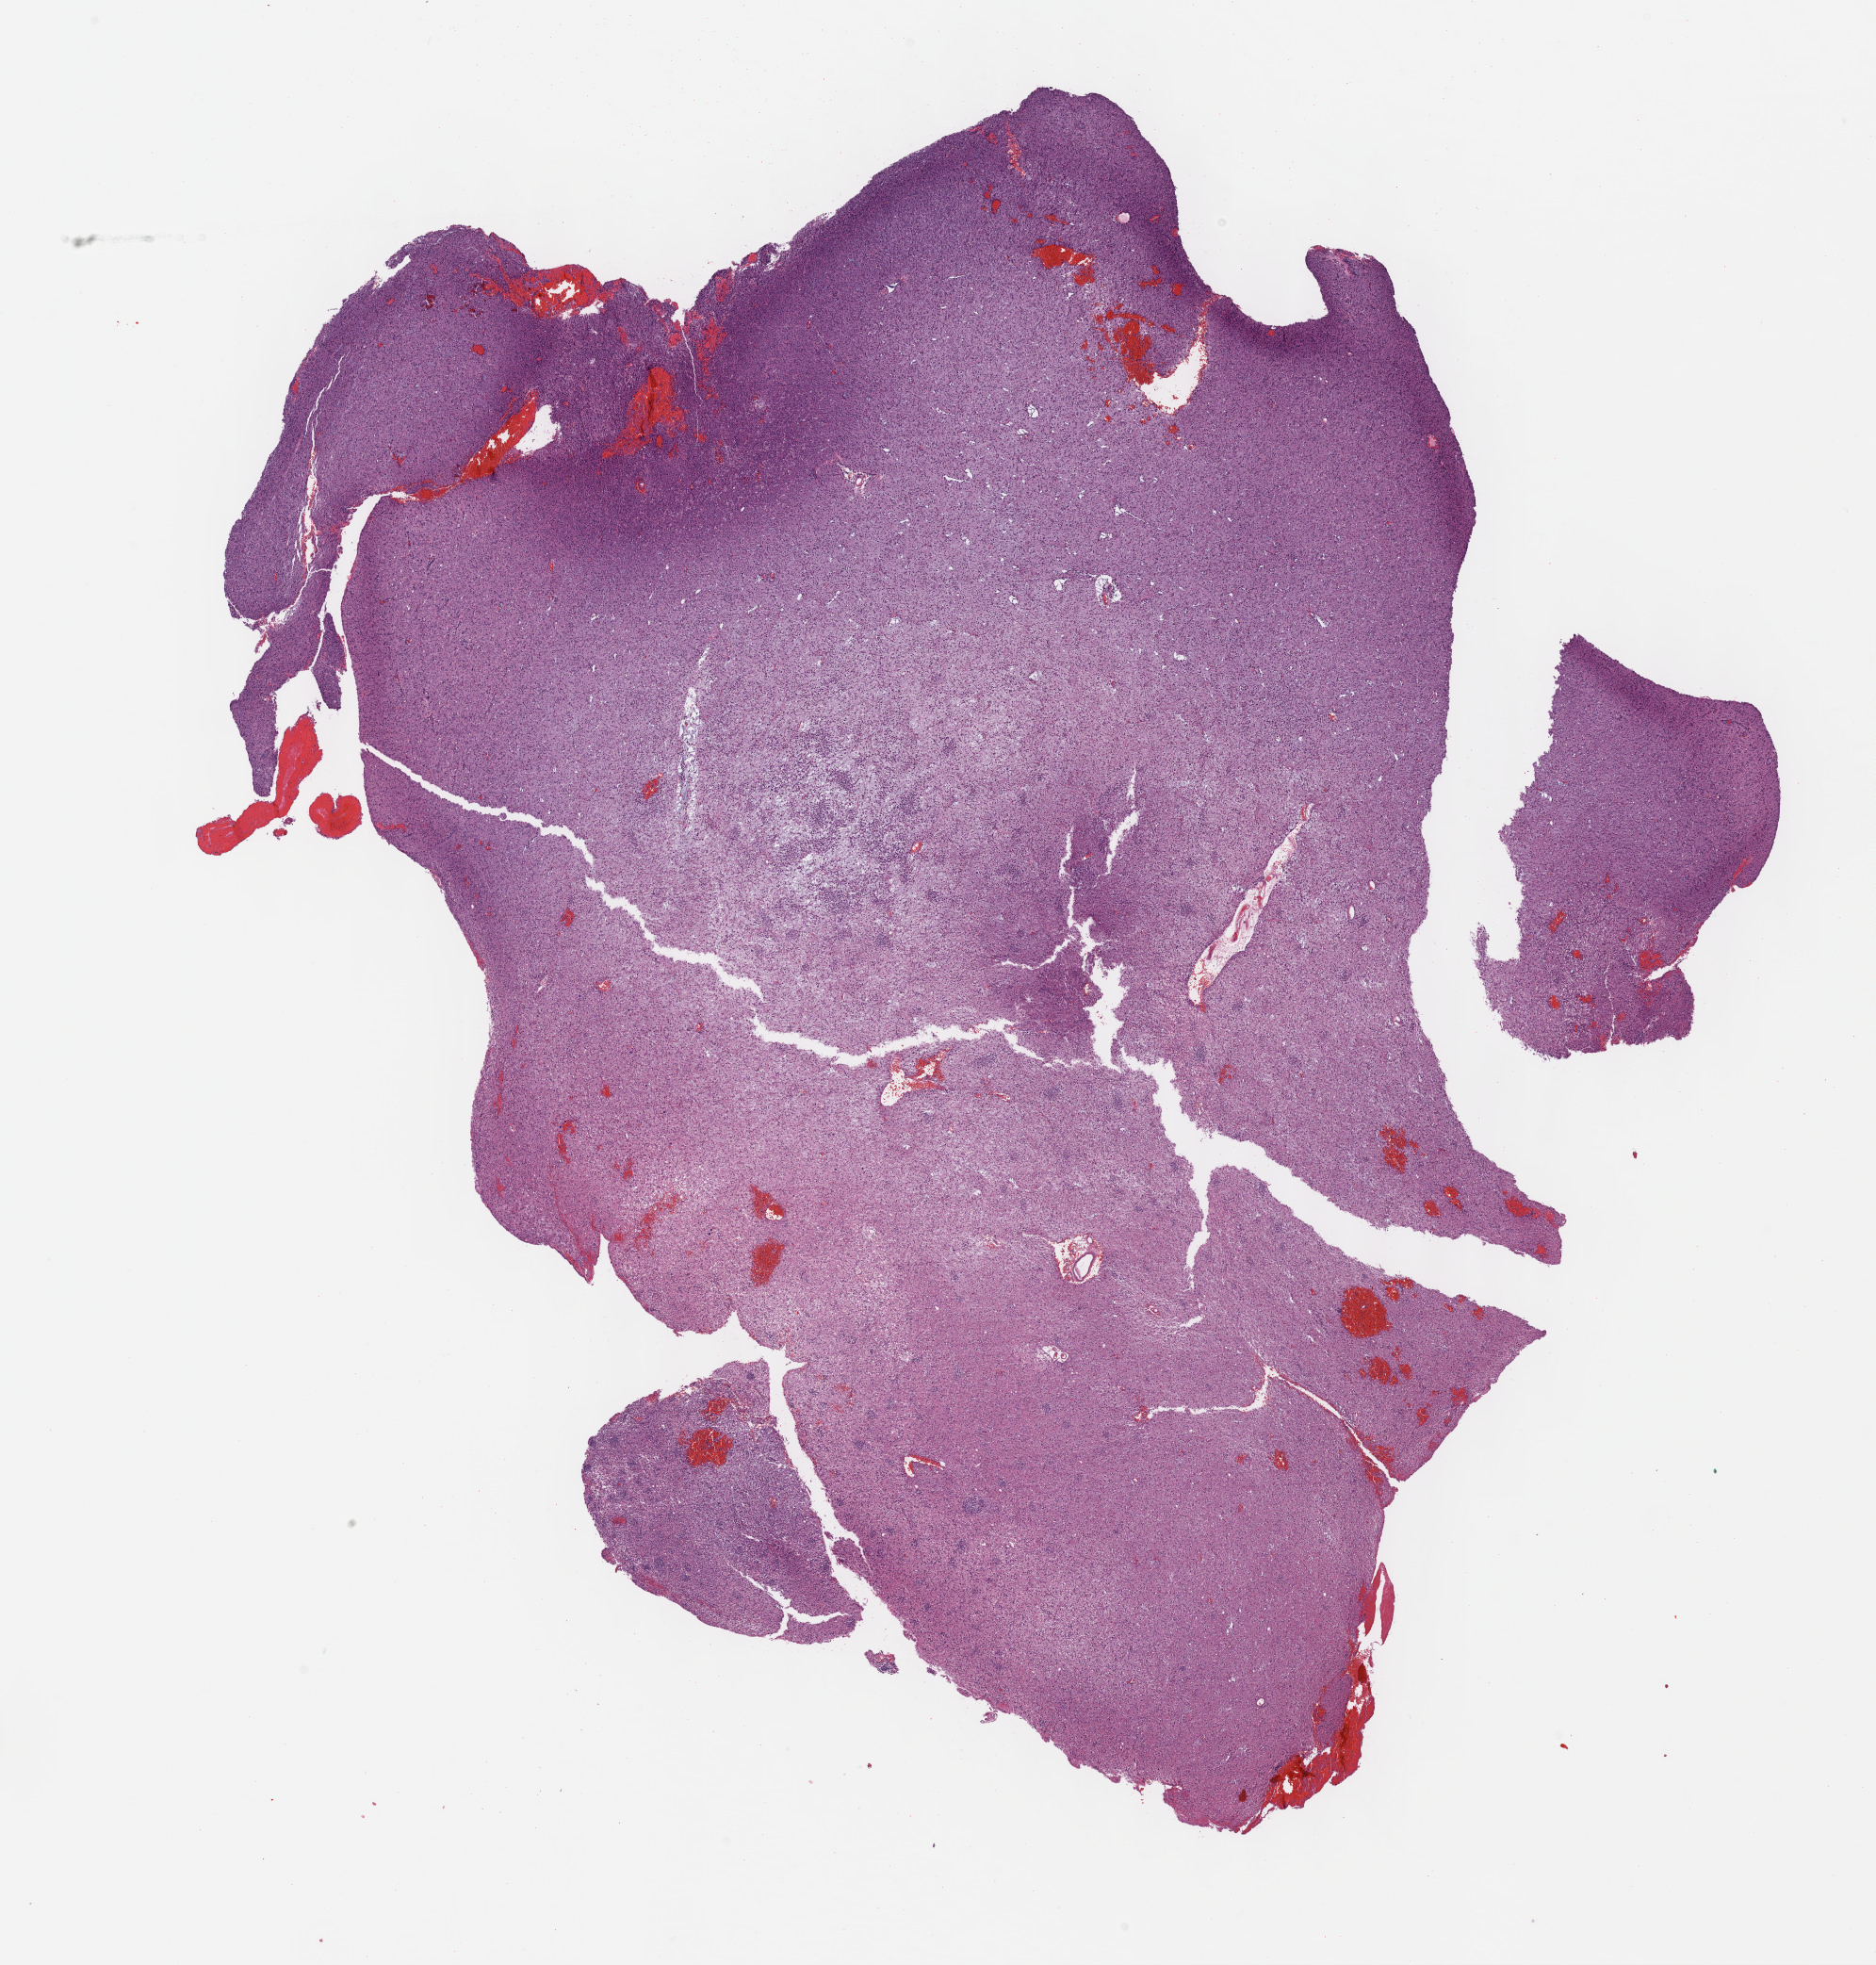
Whole-slide histology image, H&E — whole scanned area (about 16.1 x 16.9 mm) shown as a low-resolution overview; formalin-fixed paraffin-embedded (FFPE) diagnostic section; sample: primary tumour, brain. Male patient; age at initial diagnosis 67 years. Histologic grade: G3 (poorly differentiated).
Diagnosis: Mixed glioma. Laterality: right.